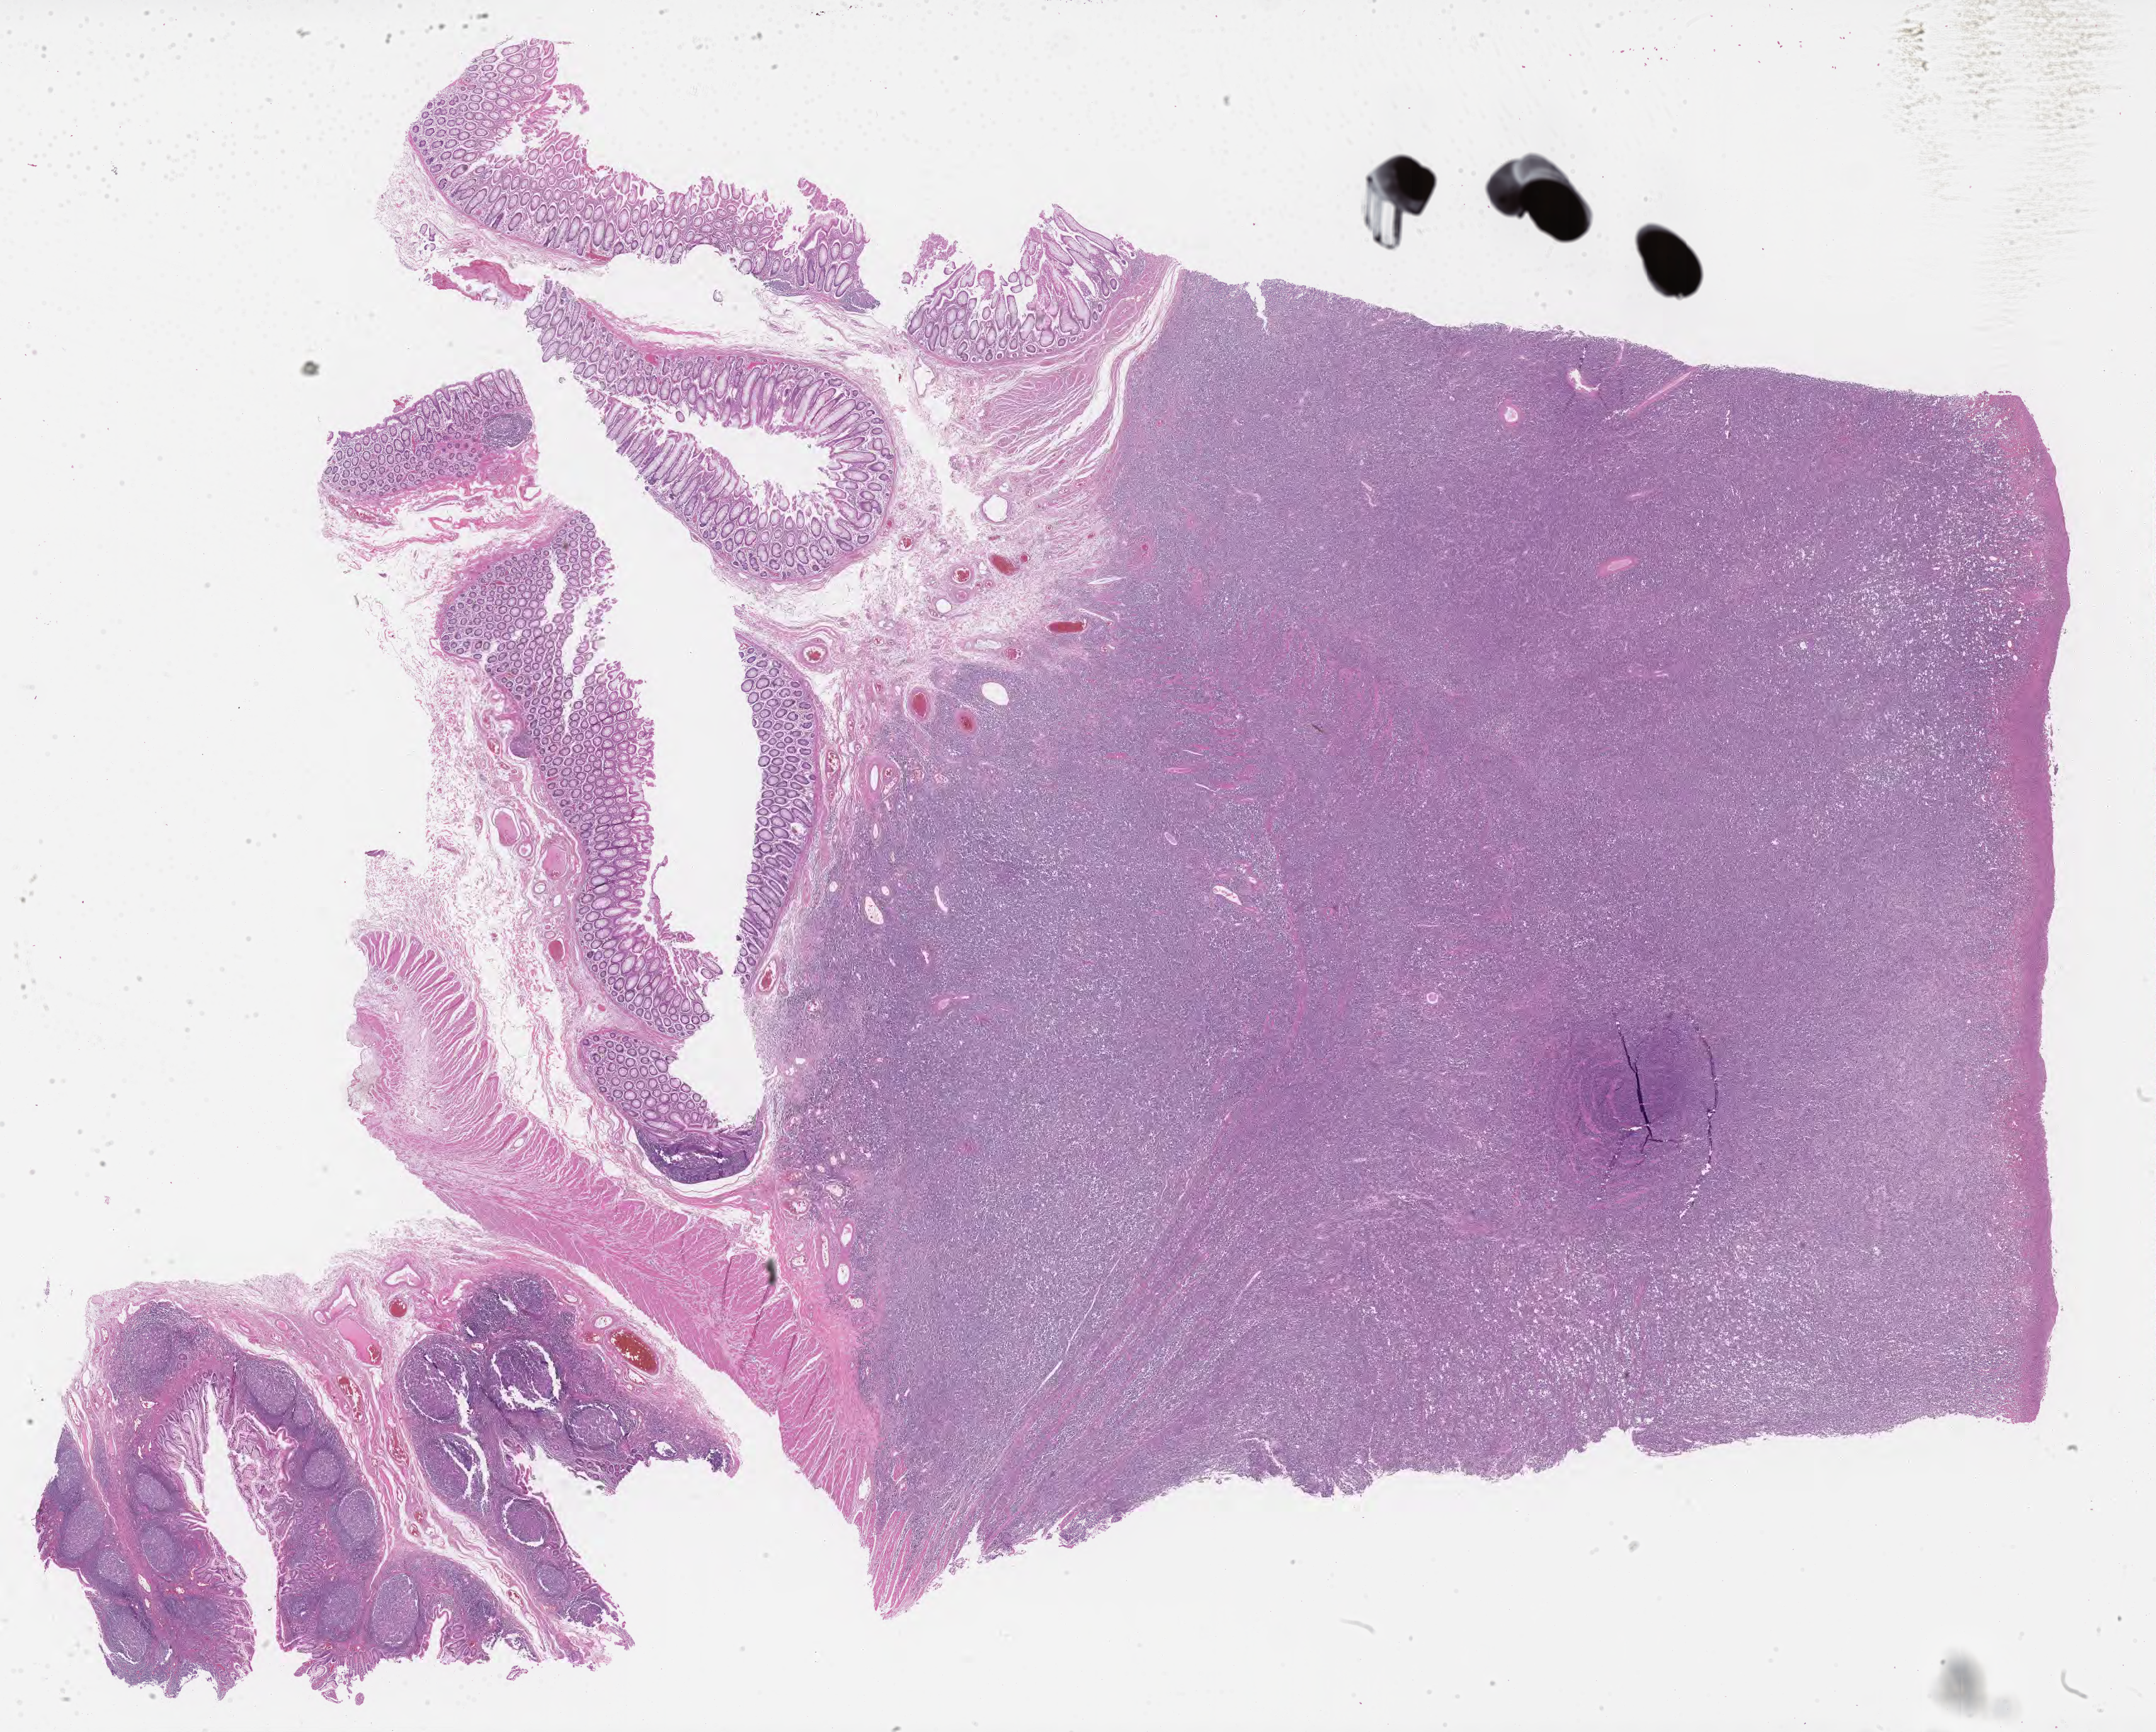
Whole-slide image, hematoxylin and eosin (H&E) stain — a low-resolution overview of the entire scanned area, about 27.7 x 22.2 mm. Tumor tissue. Male, age 7 years at initial diagnosis.
Diagnosis: Burkitt lymphoma, NOS.